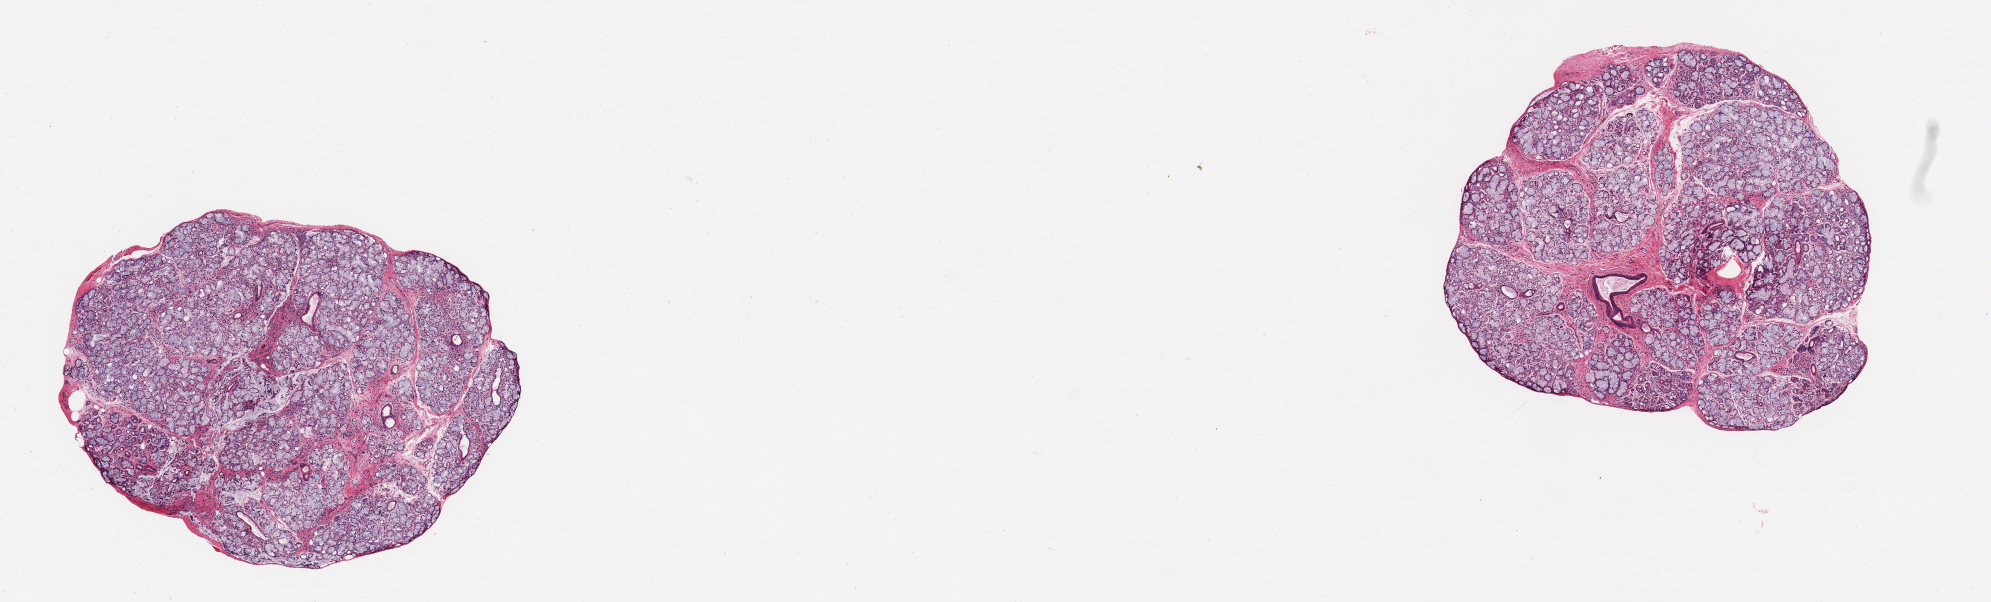
Whole-slide image, hematoxylin and eosin (H&E) stain — a low-resolution overview of the entire scanned area, about 15.8 x 4.8 mm, PAXgene-fixed paraffin-embedded (PFPE) section, target tissue: minor salivary gland, donor tissue sample. Donor sex: male.
- pathologist's review note for this sample: 2 pieces; well dissected; no extraneous tissue